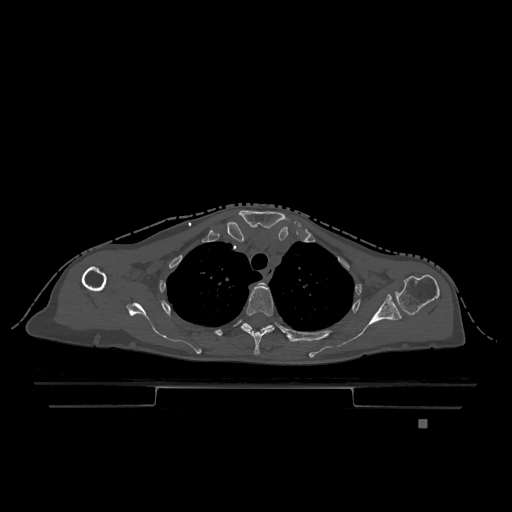
CT including the spine, one axial slice. Slice 914 of 1317 in the series (ordered by position). Bone window (W 1800 / L 400 HU). 512 × 512 image matrix. Patient: female, 74 years. From the clinical record (not read from this slice): primary cancer: lung; vertebrae with lytic lesions (as recorded): T1, T4, T5, T6, L4, L5.
Outlined on this slice (semi-automatically segmented with operator editing):
- T2 vertebra: bounding box <260,283,264,284> (left, top, right, bottom; pixels)
- T3 vertebra: <241,284,275,355>
- T4 vertebra: <243,323,307,342>